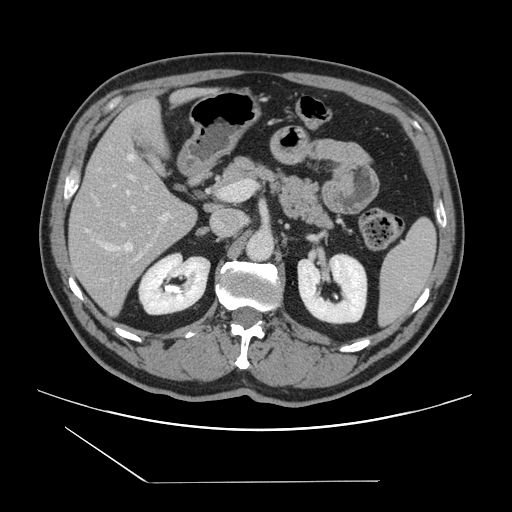
Contrast-enhanced abdominal CT, one axial slice; slice 75 of 157 in the series (ordered by position); 120 kVp; intravenous contrast given; soft-tissue window (W 400 / L 40 HU); 2.5 mm slice thickness; 512 × 512 image matrix, field of view 407 × 407 mm. Male patient, age 61 years. From the clinical record (not read from this slice): diagnosis: colorectal cancer liver metastases, imaged before liver resection; multiple liver metastases: yes; largest metastasis: 5.5 cm; disease in both lobes: yes.
Outlined on this slice (manually delineated by an expert):
- hepatic veins: bounding box (x1, y1, x2, y2) in pixels: (86, 154, 134, 251)
- liver: (70, 91, 196, 315)
- planned liver remnant (the part of the liver to remain after resection): (72, 92, 196, 220)
- portal vein (with intrahepatic branches): (122, 175, 170, 226)